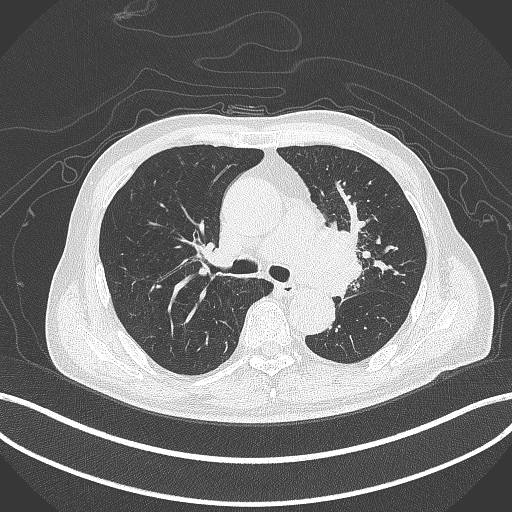
Chest CT, one axial slice. Position 275 of 417 along the scan axis. Reconstruction kernel B70f. 120 kVp. Lung window (W 1500 / L -600 HU). 1 mm slice thickness. 512 × 512 image matrix, field of view 400 × 400 mm. Patient: male, 77 years. Case-level facts recorded for this patient, not image findings: clinical TNM (as recorded): T3 N1 M0.
Annotated regions visible in this slice (rectangle marked by the reading radiologist):
- lung tumour (recorded histology: adenocarcinoma): box from (x=315, y=221) to (x=374, y=302) px